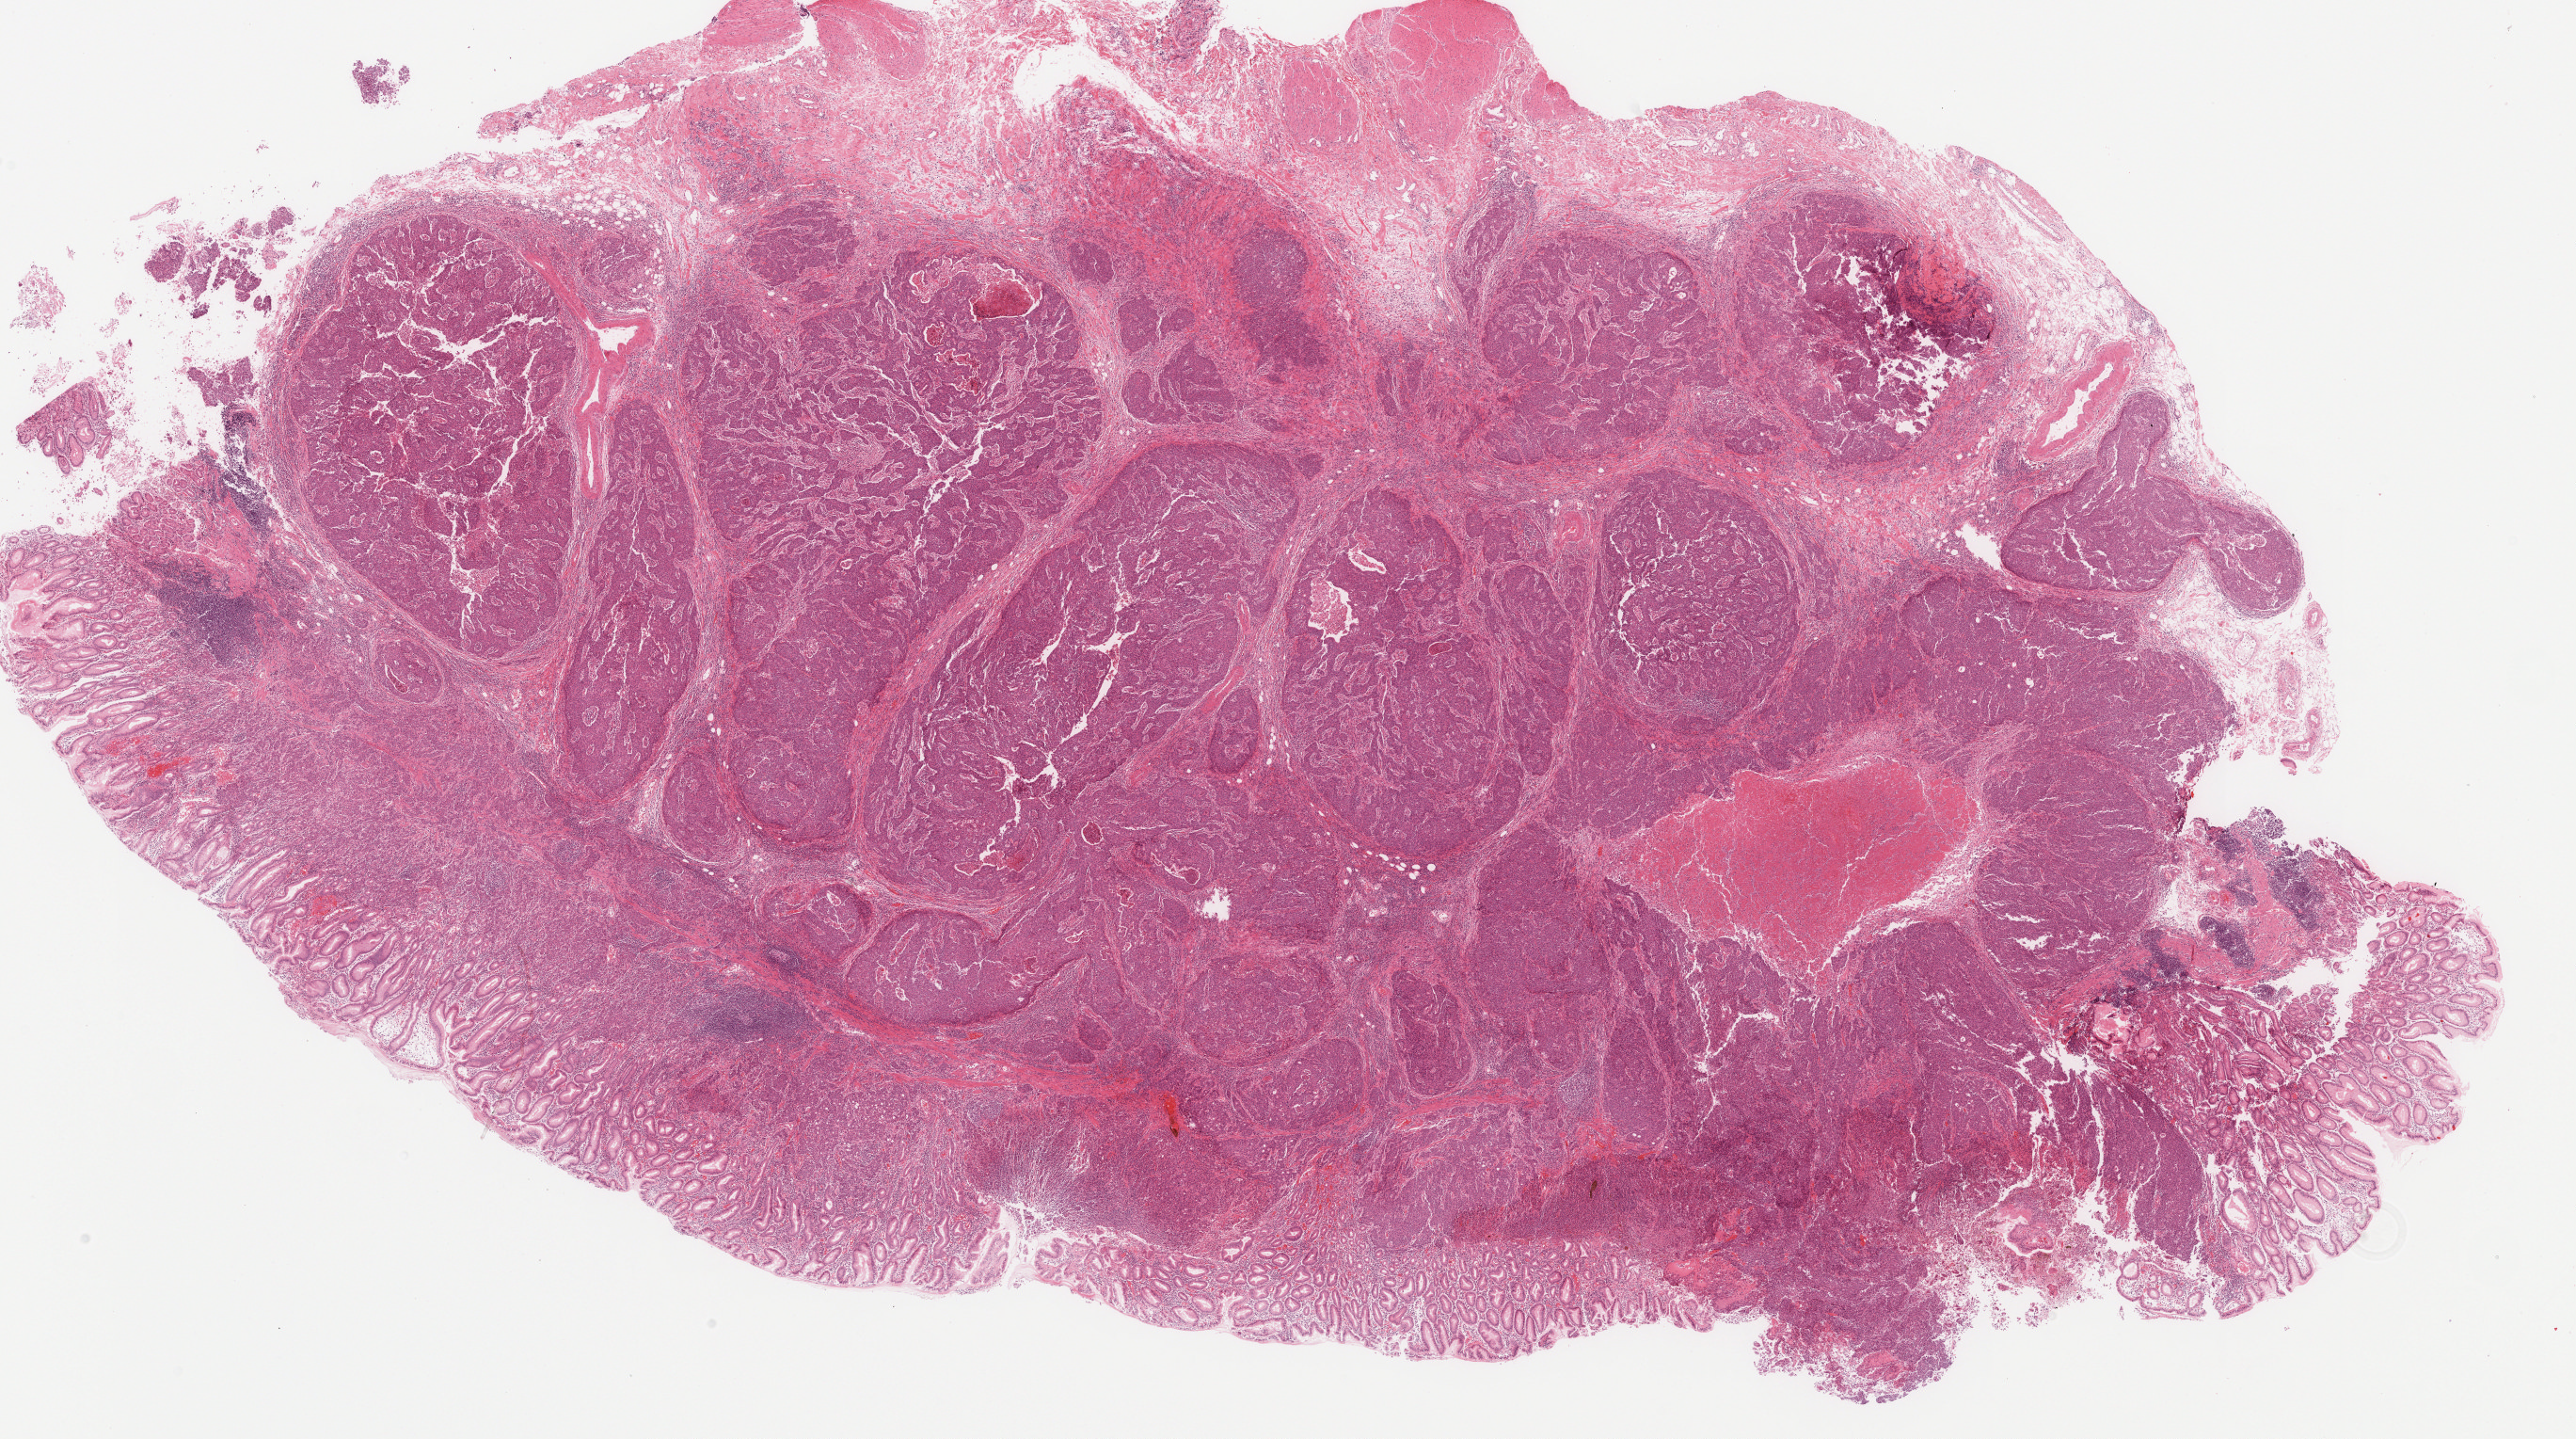
Digitized H&E tissue section (whole slide), low-resolution overview of the scanned area, about 21.6 x 12.1 mm (acquisition: 20x scan); FFPE section; sample: primary tumour, stomach. Female patient; age at initial diagnosis 70 years. Histologic grade: G3 (poorly differentiated).
Diagnosis: Carcinoma, diffuse type (gastric antrum). AJCC pathologic stage: IIIC (7th edition).